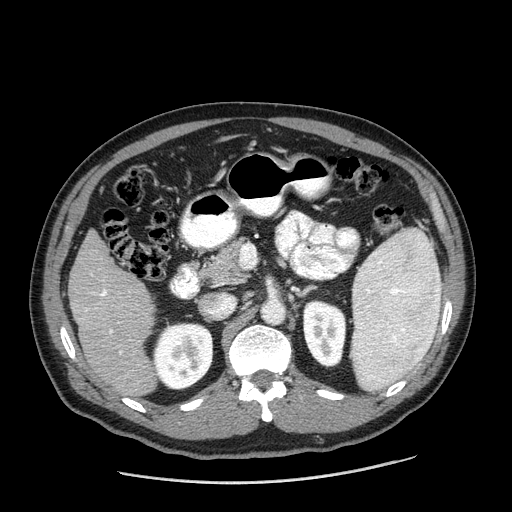
Contrast-enhanced abdominal CT (liver protocol), one axial slice; slice 83 of 198 in the series (ordered by position); reconstruction kernel STANDARD; 120 kVp; one of 2 acquisitions stored at this slice position; soft-tissue window (W 400 / L 40 HU); 2.5 mm slice thickness; 512 × 512 image matrix, field of view 400 × 400 mm. Case-level facts recorded for this patient, not image findings: diagnosis: hepatocellular carcinoma (patient treated with transarterial chemoembolisation; whether this scan precedes or follows treatment is not stated here); TNM stage (as recorded): Stage-II; Child-Pugh class: A; tumour size: 2.6 cm.
Outlined on this slice (semi-automatically segmented with operator editing):
- liver parenchyma outside the tumour (the mass and vessels are separate outlines, so this box may not span the whole liver): bounding box (x1, y1, x2, y2) in pixels: (68, 230, 156, 396)
- liver vessels: (85, 290, 122, 354)